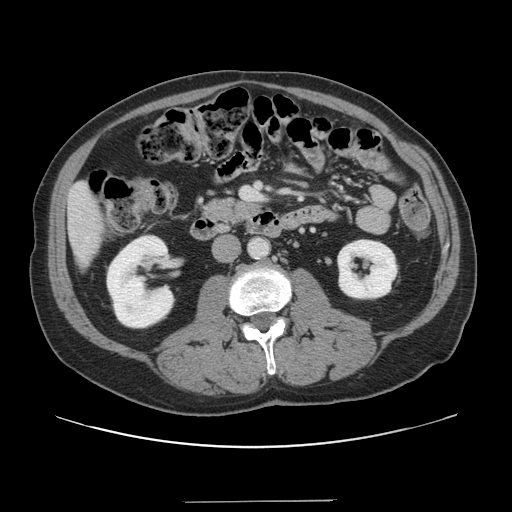
Contrast-enhanced abdominal CT, one axial slice. Position 43 of 151 along the scan axis. 120 kVp. Intravenous contrast given. Soft-tissue window (W 400 / L 40 HU). 2.5 mm slice thickness. 512 × 512 image matrix. Male patient, age 63 years. From the clinical record (not read from this slice): diagnosis: colorectal cancer liver metastases, imaged before liver resection; multiple liver metastases: no; largest metastasis: 2.1 cm; disease in both lobes: no.
Structures marked on this image (expert manual segmentation):
- liver: bounding box (x1, y1, x2, y2) in pixels: (69, 184, 104, 264)
- planned liver remnant (the part of the liver to remain after resection): (69, 184, 104, 265)
- portal vein (with intrahepatic branches): (243, 188, 261, 199)